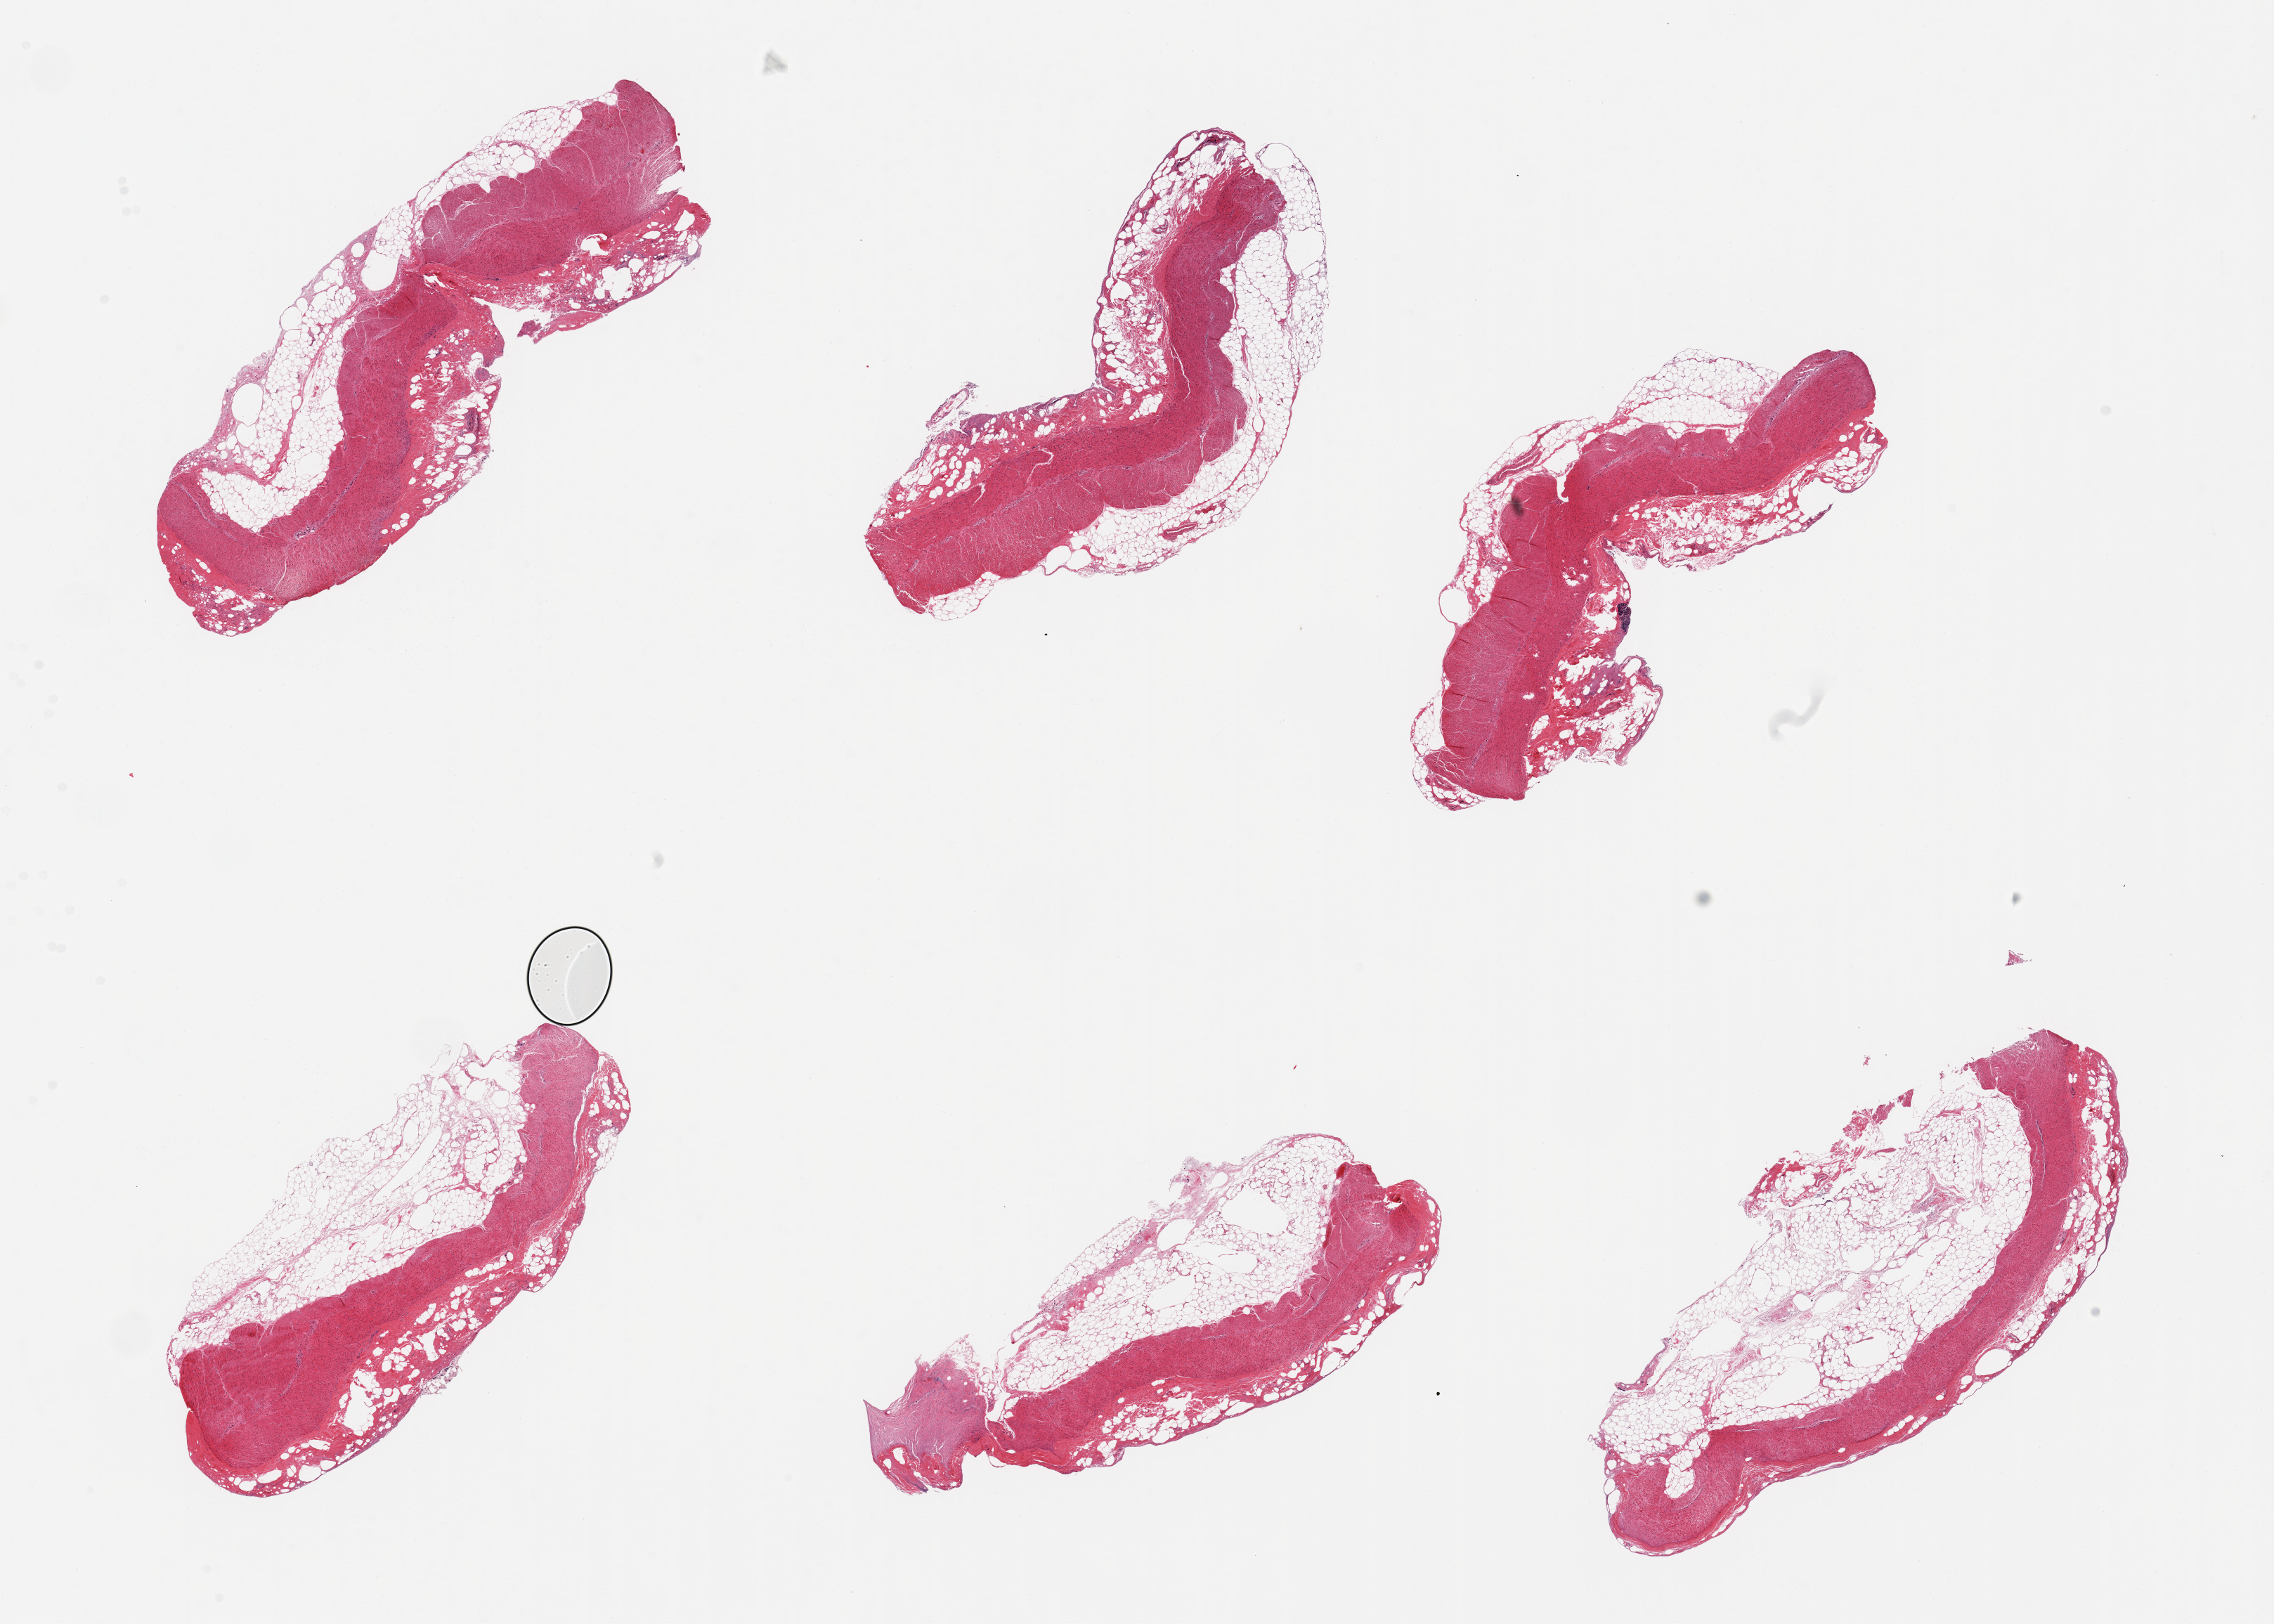
Whole-slide image, haematoxylin and eosin stain — whole scanned area (about 25.6 x 18.3 mm, acquisition: 20x scan) shown as a low-resolution overview, PAXgene-fixed paraffin-embedded (PFPE) section, section of sigmoid colon (target tissue), donor tissue sample.
- reviewer comment on this tissue sample: 6 pieces; large amount of fat on both sides (adventitia and submucosa) measuring up to 2.5 mm and thicker than the muscularis